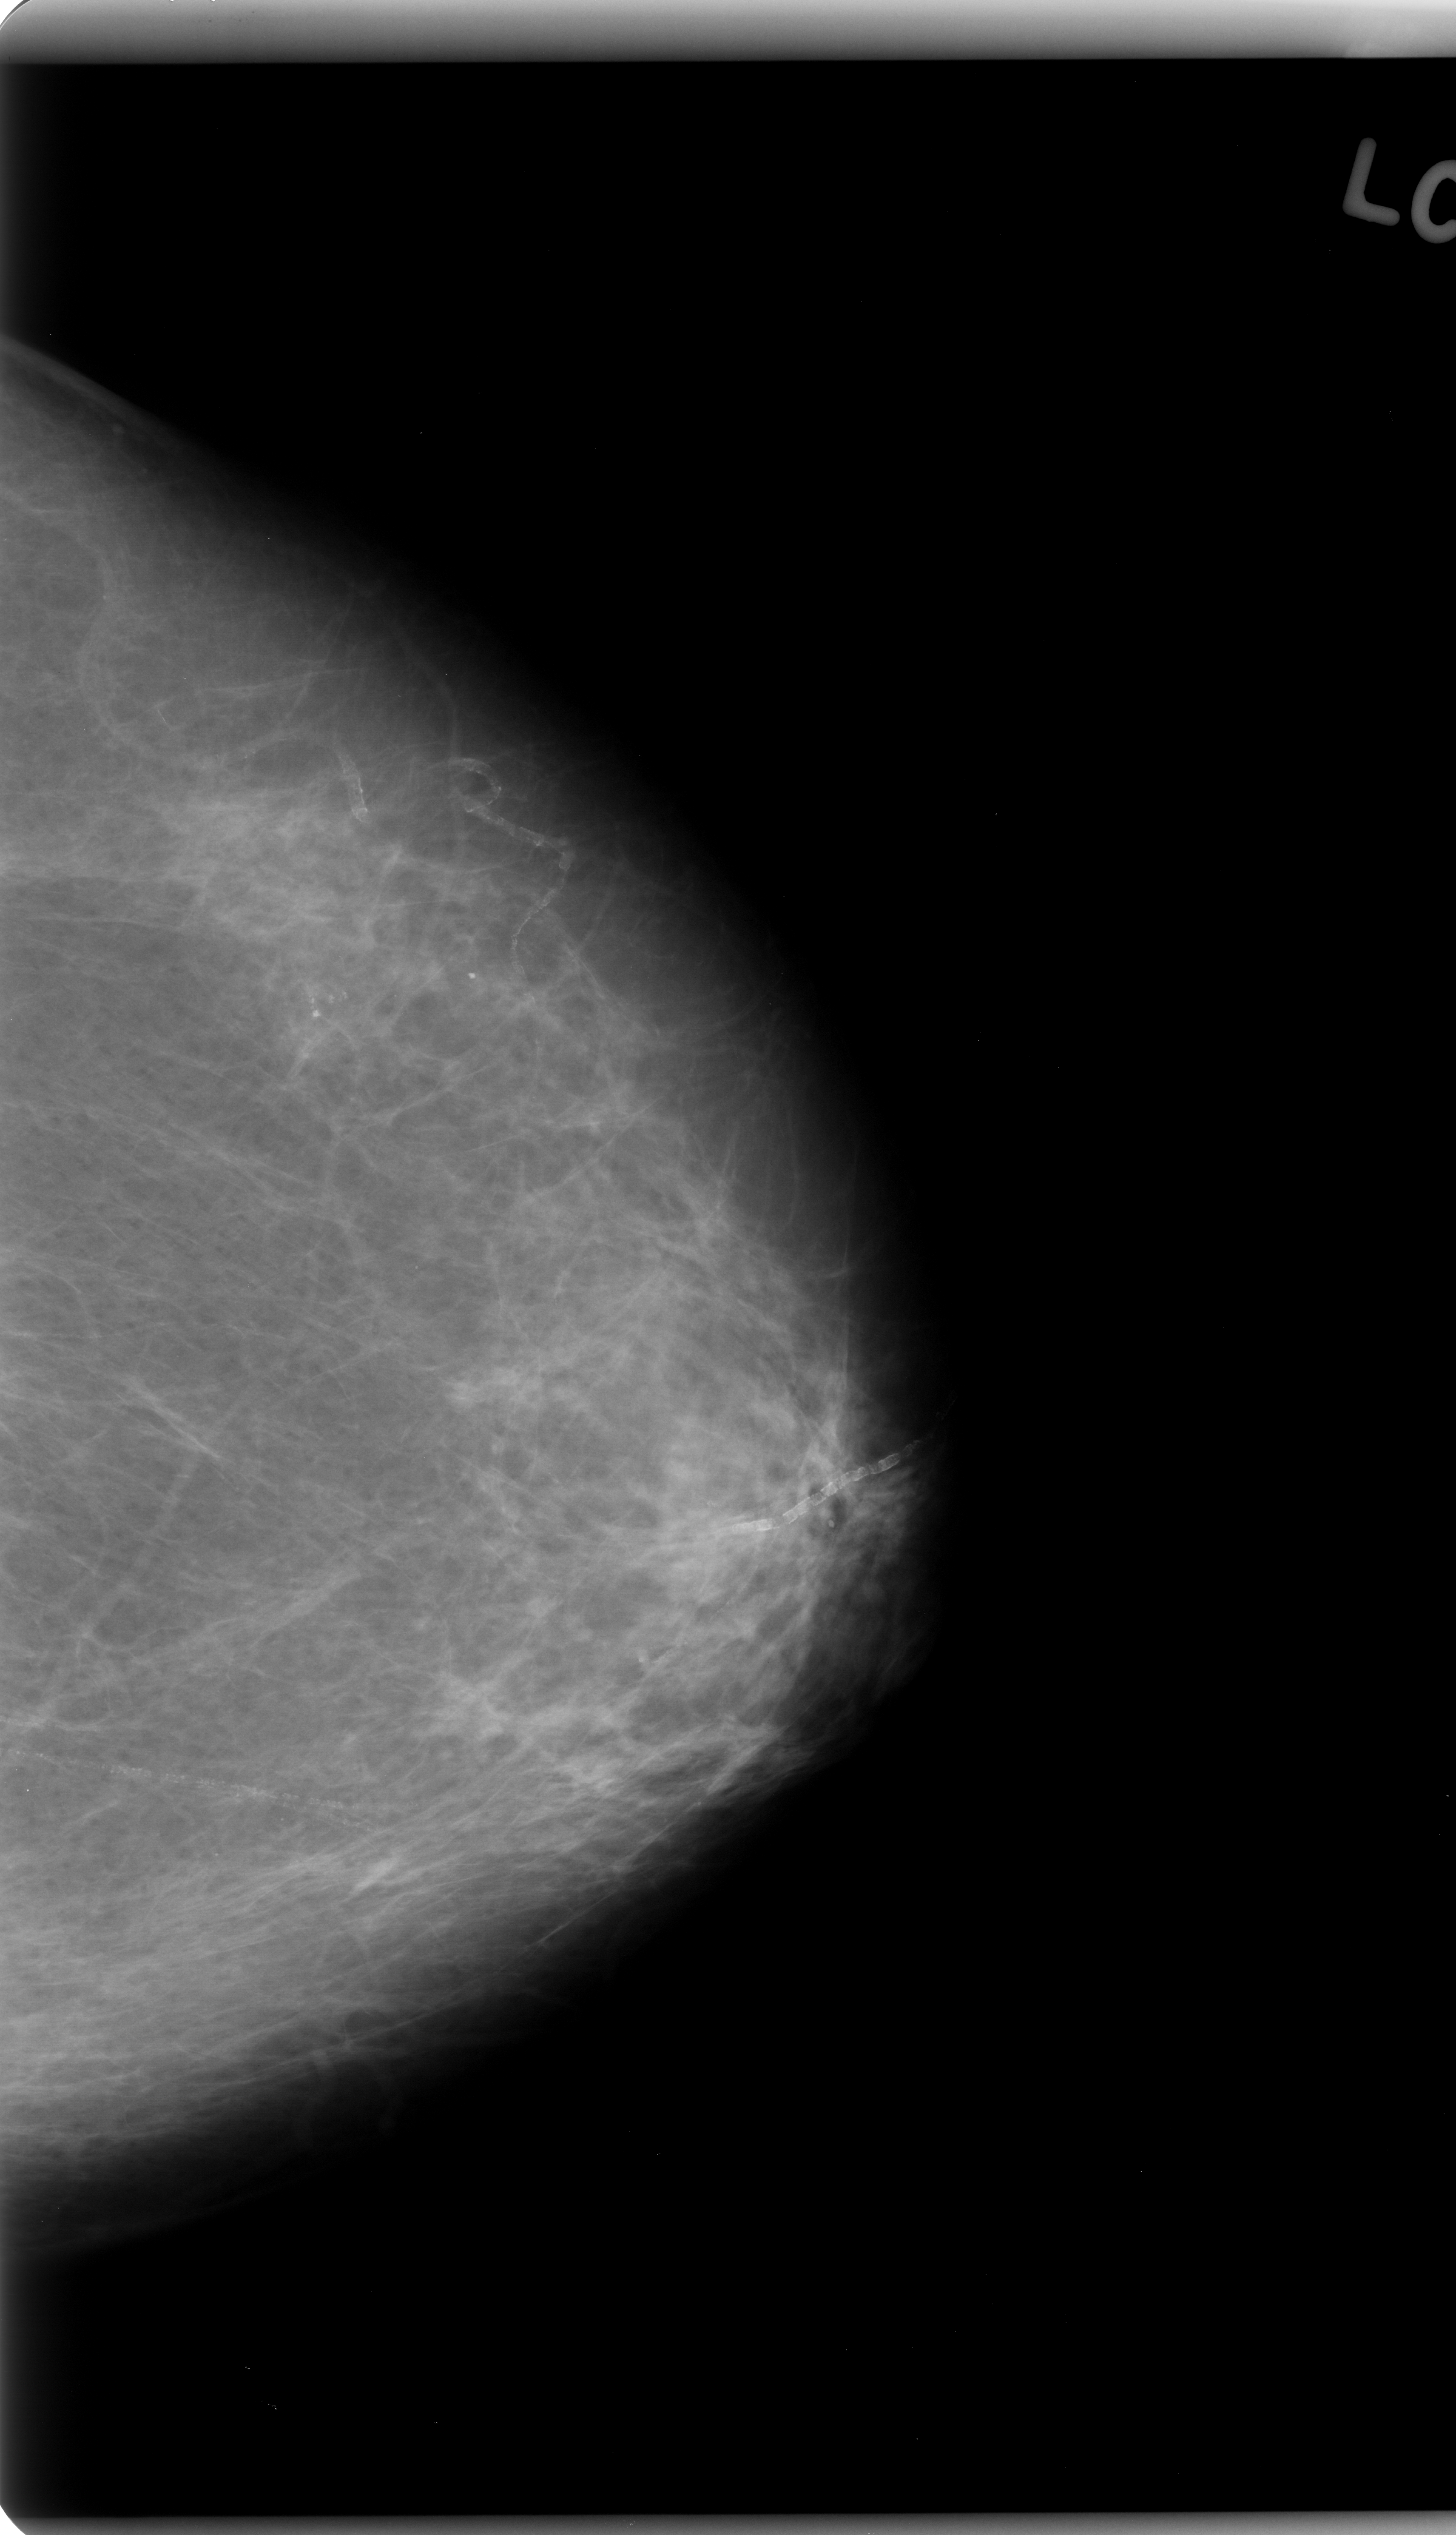
Digitized screen-film mammogram; left breast; craniocaudal (CC) view; BI-RADS breast density category 1 (scale 1–4); 1456 × 2535 image matrix.
Marked abnormalities (boxes around the expert regions of interest):
- calcifications, morphology pleomorphic, distribution clustered; BI-RADS assessment category 4; subtlety rating 5 on a 1 (subtle) to 5 (obvious) scale; pathology (as recorded): benign: bounding box <268,969,365,1059> (left, top, right, bottom; pixels)